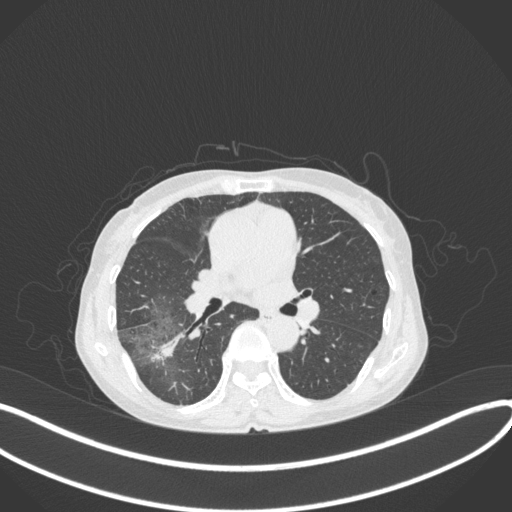
Chest CT, one axial slice; position 216 of 379 along the scan axis; 120 kVp; lung window (W 1500 / L -600 HU); 1 mm slice thickness; 512 × 512 image matrix, field of view 400 × 400 mm. Female patient, age 69 years. Case-level facts recorded for this patient, not image findings: clinical TNM (as recorded): T1b N0 M0; histopathological grade: G2-3.
Outlined on this slice (rectangle marked by the reading radiologist):
- lung tumour (recorded histology: adenocarcinoma): bounding box (x1, y1, x2, y2) in pixels: (146, 326, 186, 370)